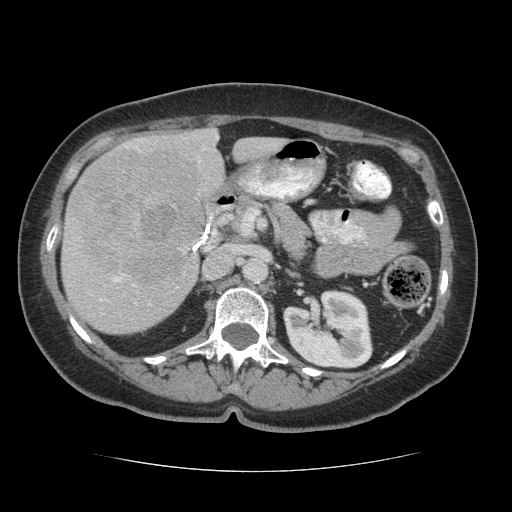
Contrast-enhanced abdominal CT (liver protocol), one axial slice; position 29 of 75 along the scan axis; reconstruction kernel STANDARD; 140 kVp; soft-tissue window (W 400 / L 40 HU); 512 × 512 image matrix, field of view 360 × 360 mm. From the clinical record (not read from this slice): diagnosis: hepatocellular carcinoma (patient treated with transarterial chemoembolisation; whether this scan precedes or follows treatment is not stated here); TNM stage (as recorded): Stage-I; Child-Pugh class: A; tumour differentiation: moderately differentiated; tumour nodularity: uninodular.
Structures marked on this image (semi-automatically segmented with operator editing):
- liver parenchyma outside the tumour (the mass and vessels are separate outlines, so this box may not span the whole liver): bounding box (x1, y1, x2, y2) in pixels: (62, 128, 285, 332)
- mass: (68, 148, 208, 288)
- liver vessels: (99, 135, 219, 305)